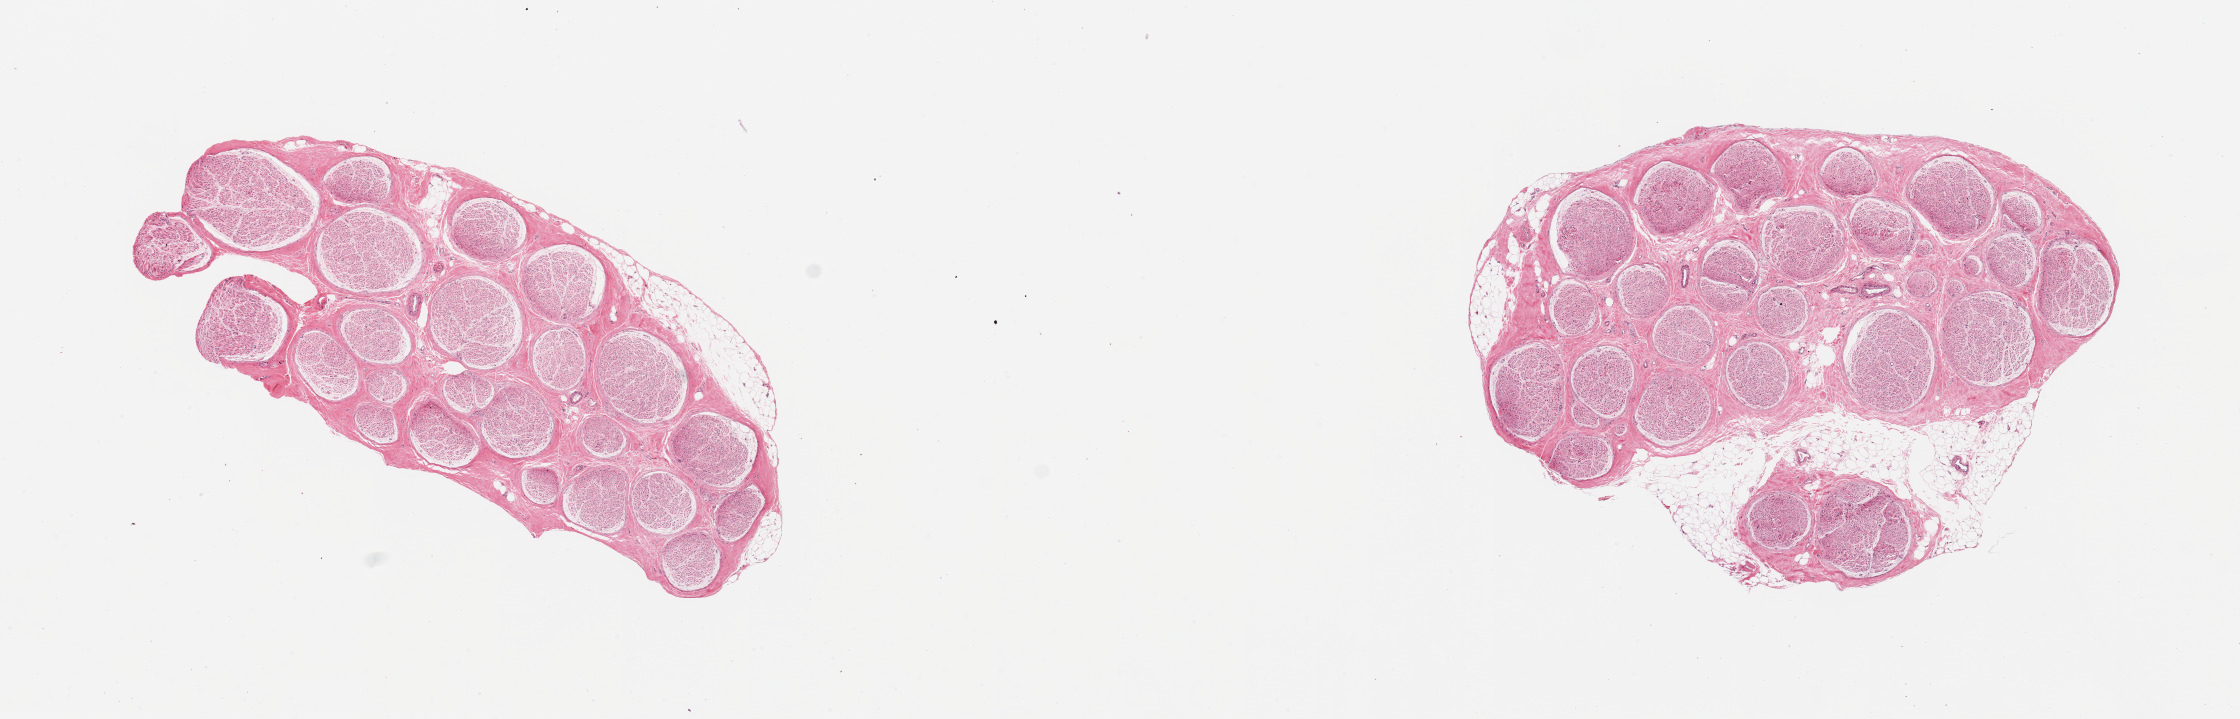
Hematoxylin and eosin (H&E) whole-slide image — low-resolution overview of the scanned area, about 17.7 x 5.7 mm. PAXgene-fixed paraffin-embedded (PFPE) section. Sampled site (target tissue): tibial nerve. Donor tissue sample.
* review note (as recorded): 2 pieces; one with ~10% external fat, other with up to 10% internal/external fat